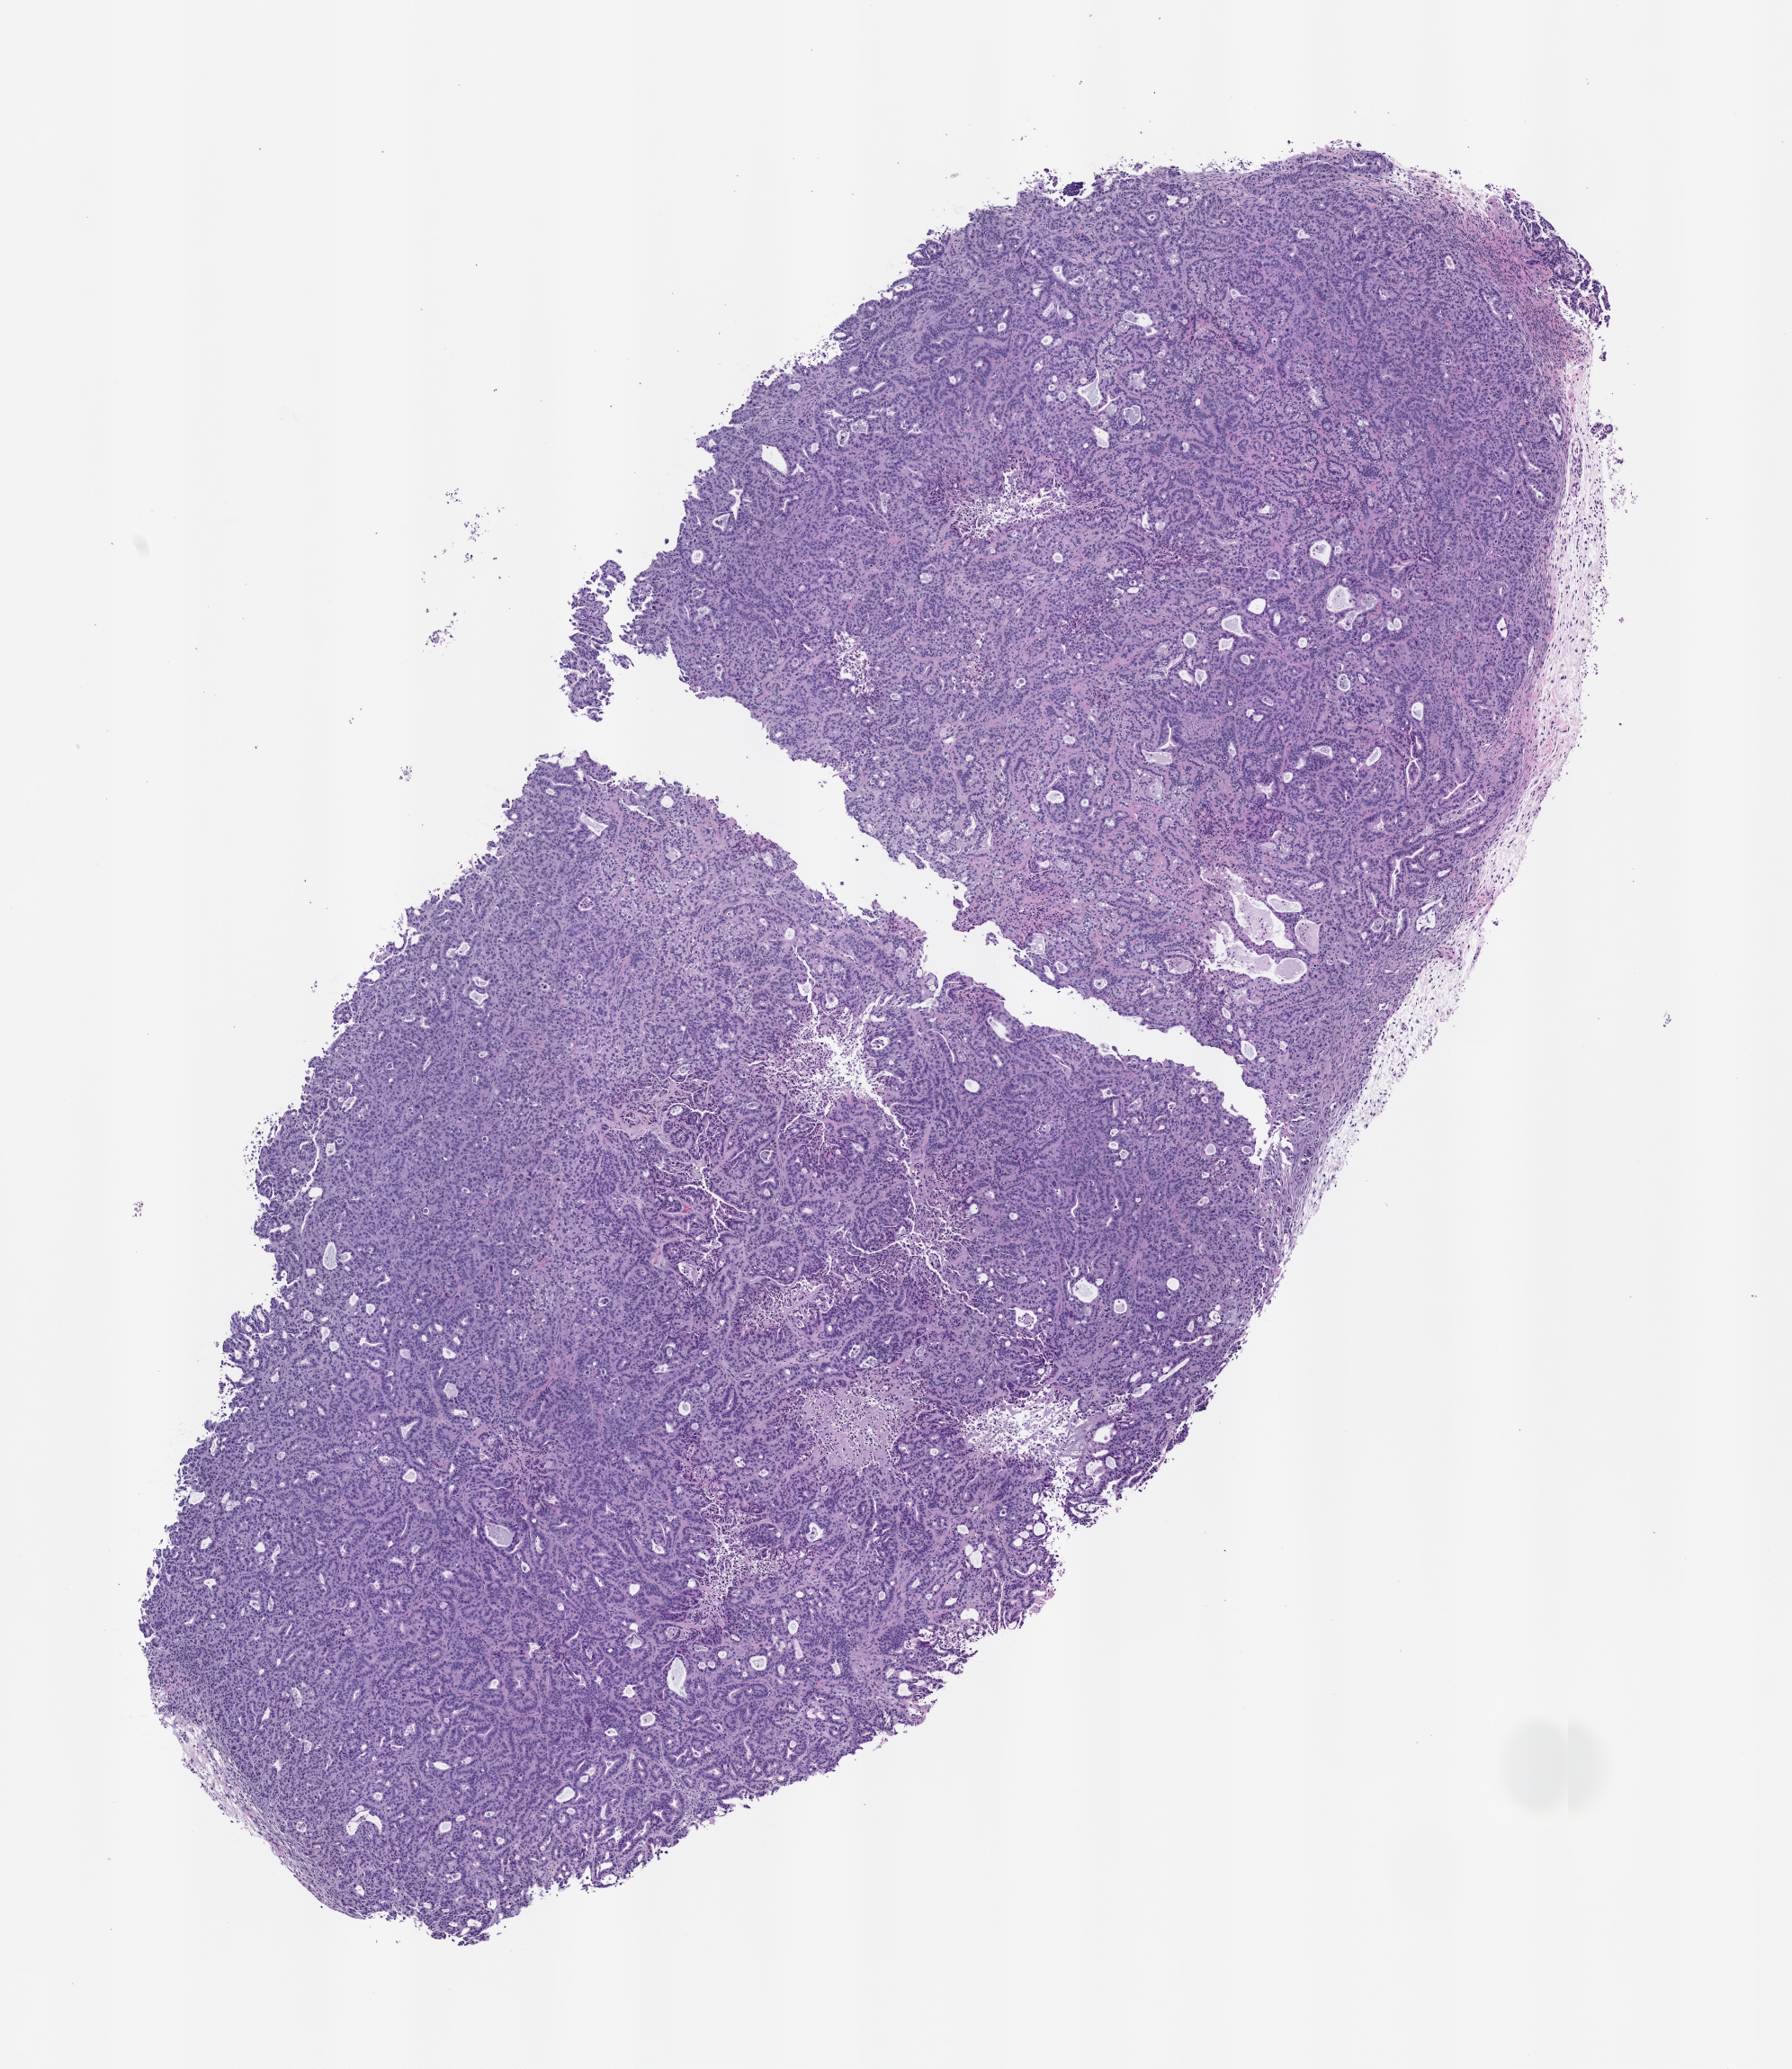
Whole-slide image, hematoxylin and eosin (H&E): patient-derived xenograft (human tumor grown in a mouse), passage 0 — low-resolution overview of the scanned area, about 8.0 x 9.2 mm, formalin-fixed paraffin-embedded section, tumor site category: pancreas.
Originating patient diagnosis: Pancreatic Adenocarcinoma.